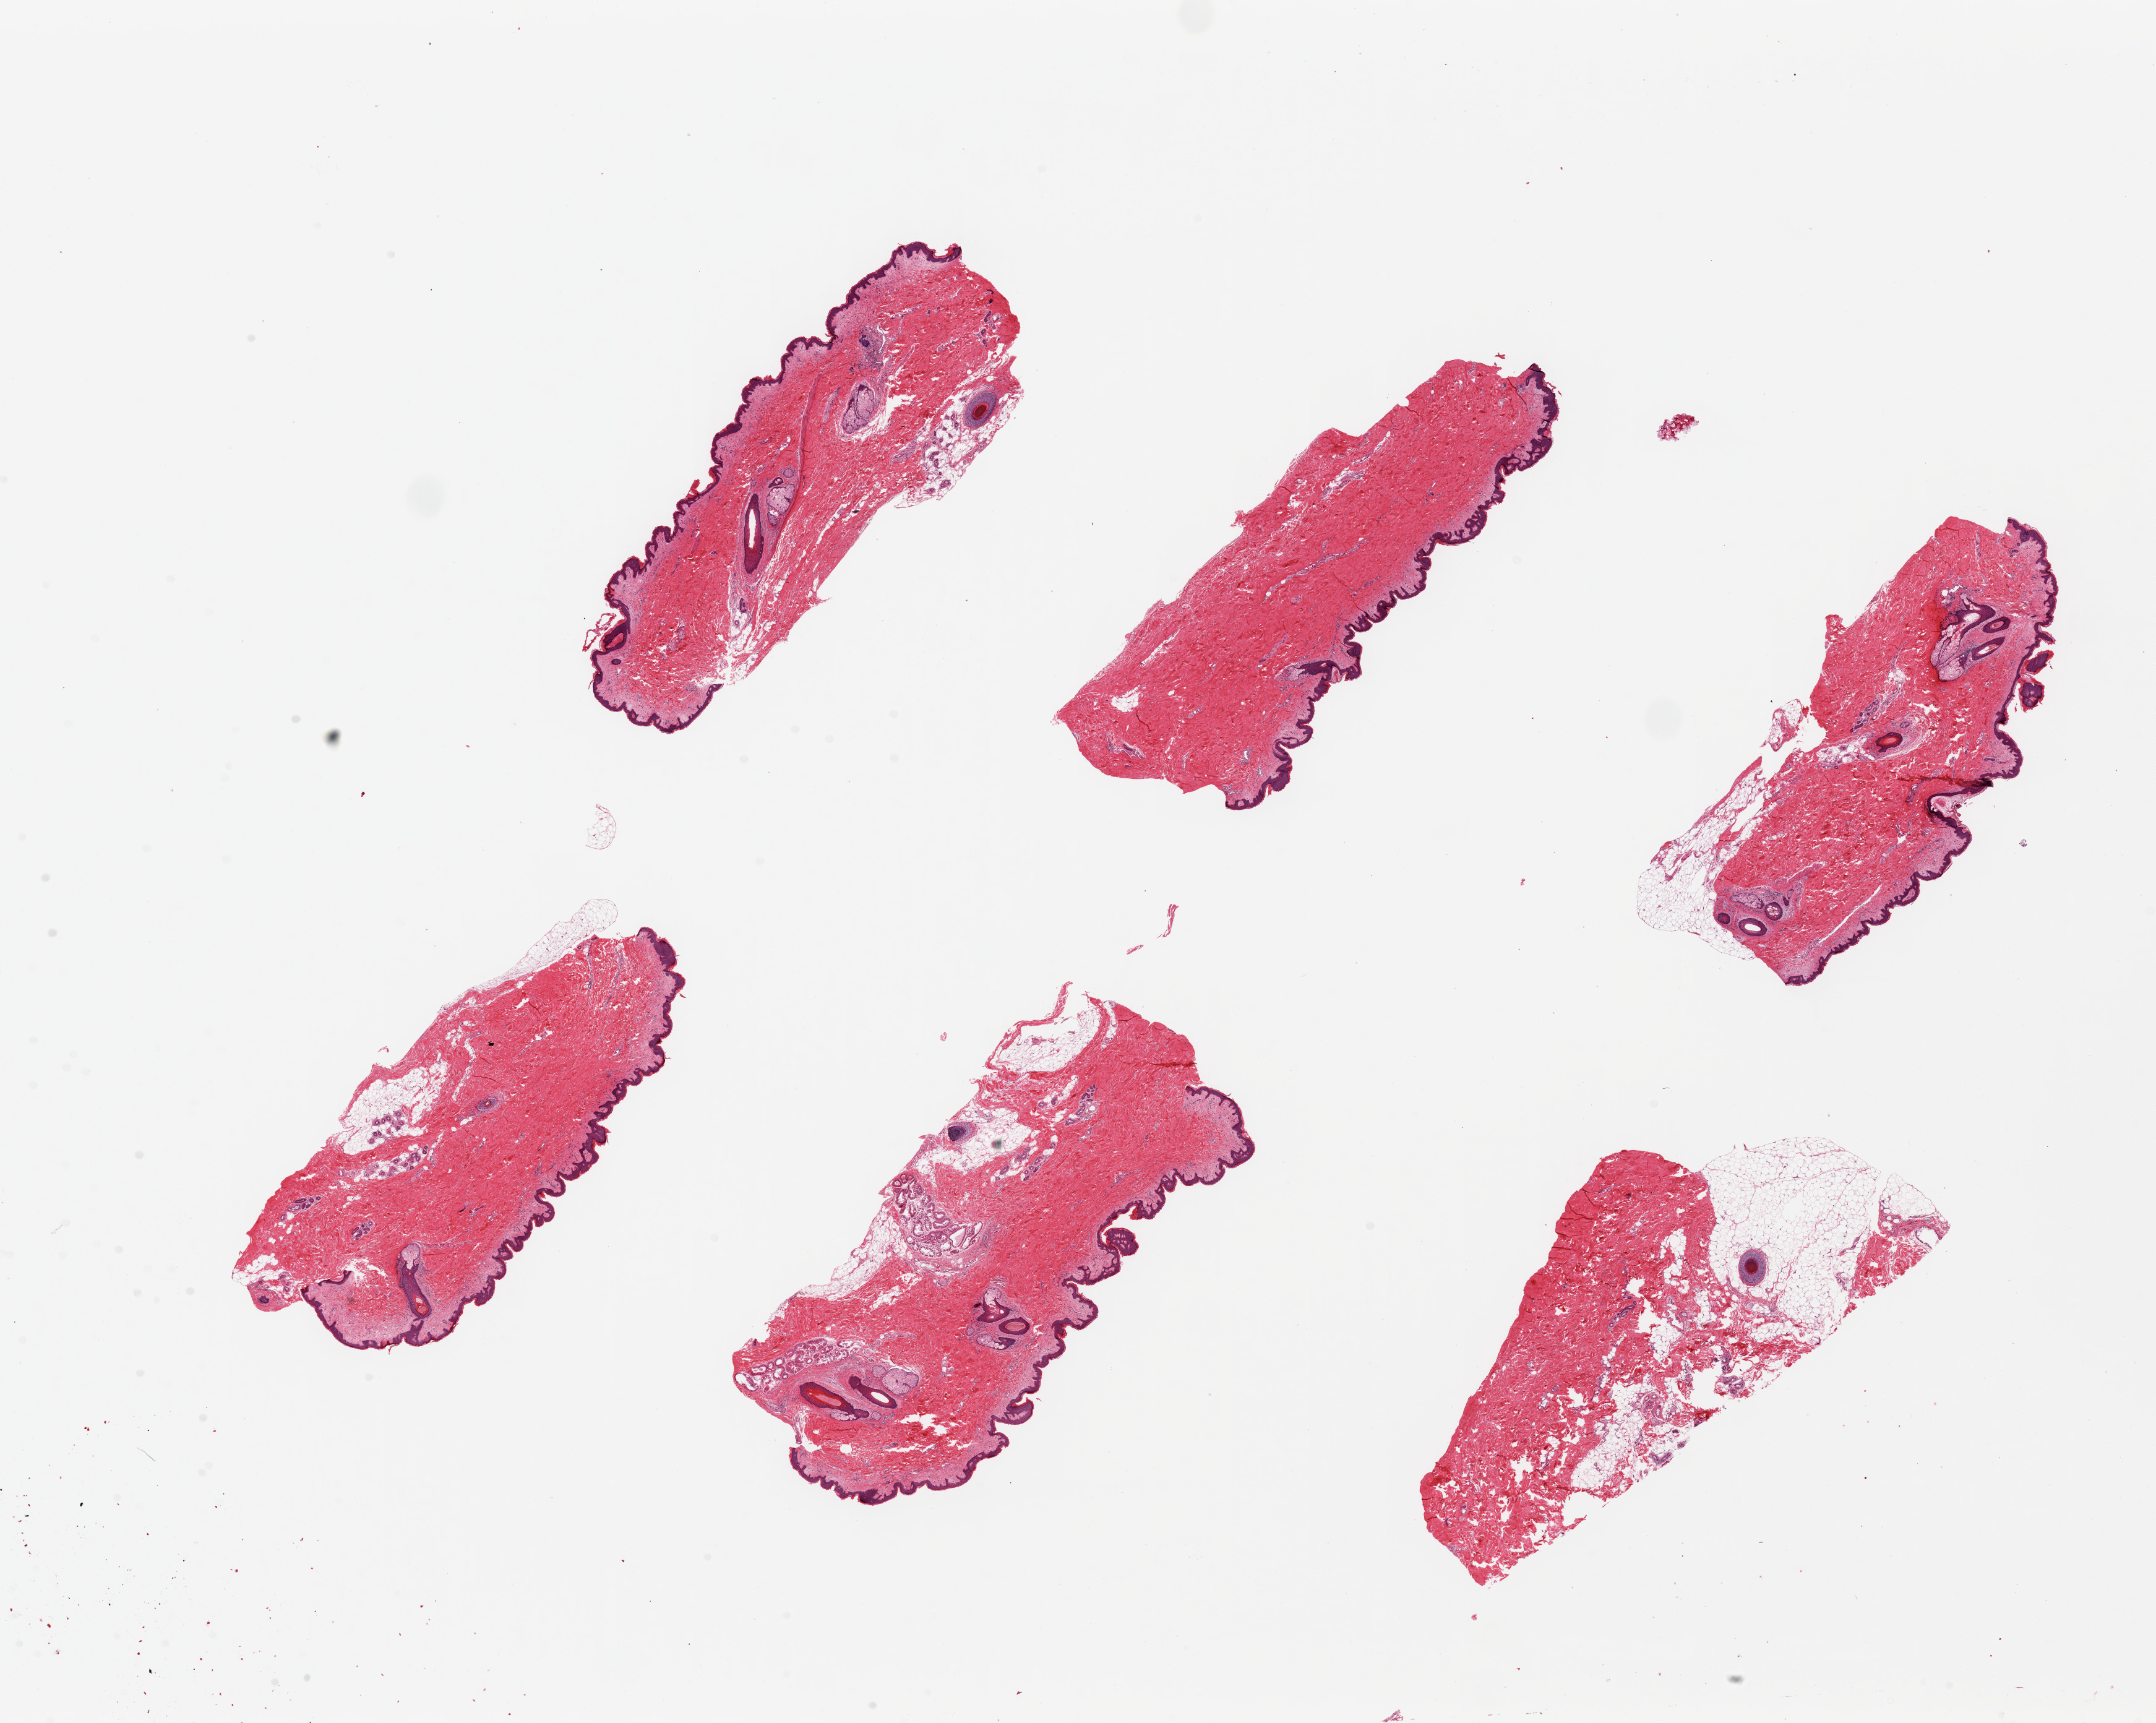
Digitized haematoxylin and eosin-stained section, shown as a low-resolution overview of the whole scanned area (about 27.6 x 22.0 mm). PAXgene-fixed, paraffin-embedded tissue. Sampled site (target tissue): skin of suprapubic region. Donor tissue sample.
* reviewer comment on this tissue sample: 6 ~7x.2.5mm pieces; squamous epithelium is ~2-3% thickness